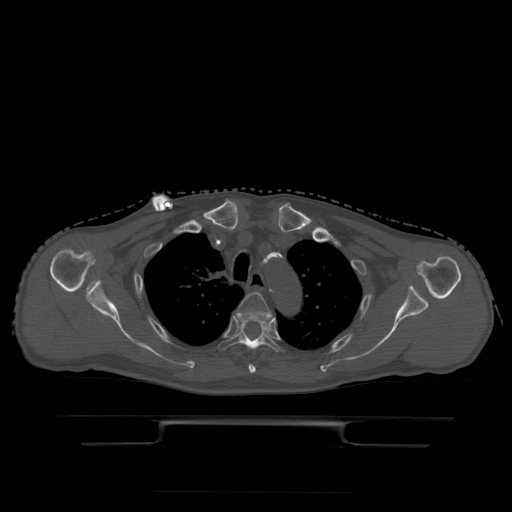
CT including the spine, one axial slice; slice 361 of 522 in the series (ordered by position); bone window (W 1800 / L 400 HU); 1.25 mm slice thickness; 512 × 512 image matrix, field of view 436 × 436 mm. Patient age 68 years. Case-level facts recorded for this patient, not image findings: primary cancer: urothelial.
Outlined on this slice (semi-automatically segmented with operator editing):
- T3 vertebra: bounding box (x1, y1, x2, y2) in pixels: (237, 293, 272, 374)
- T4 vertebra: (218, 316, 284, 352)